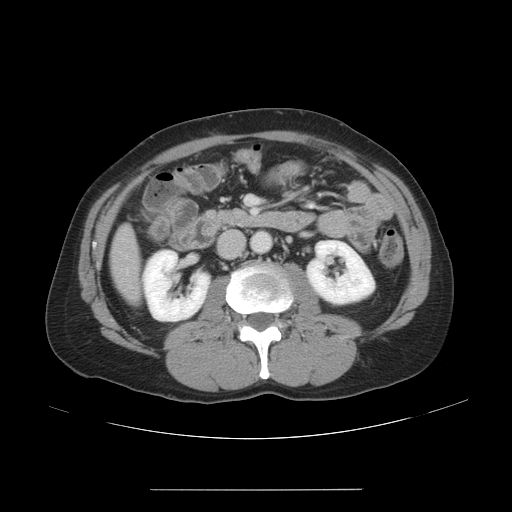
Contrast-enhanced abdominal CT, one axial slice. Position 17 of 48 along the scan axis. Reconstruction kernel STANDARD. Intravenous contrast given. Soft-tissue window (W 400 / L 40 HU). 5 mm slice thickness. 512 × 512 image matrix, field of view 409 × 409 mm. Male patient, age 56 years. From the clinical record (not read from this slice): diagnosis: colorectal cancer liver metastases, imaged before liver resection; multiple liver metastases: yes; largest metastasis: 1.8 cm.
Structures marked on this image (manually delineated by an expert):
- hepatic veins: box from (x=126, y=256) to (x=128, y=273) px
- liver: (x=113, y=228)–(x=138, y=299)
- planned liver remnant (the part of the liver to remain after resection): (x=115, y=273)–(x=138, y=299)